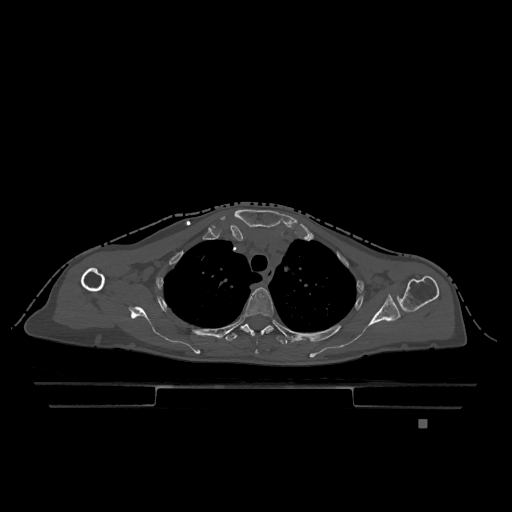
CT including the spine, one axial slice; position 908 of 1317 along the scan axis; bone window (W 1800 / L 400 HU); 0.5 mm slice thickness; 512 × 512 image matrix, field of view 500 × 500 mm. Female patient, age 74 years. From the clinical record (not read from this slice): primary cancer: lung; vertebrae with lytic lesions (as recorded): T1, T4, T5, T6, L4, L5.
Structures marked on this image (semi-automatic segmentation, software-assisted and operator-edited):
- T3 vertebra: bounding box [x1, y1, x2, y2] px = [241, 287, 274, 354]
- T4 vertebra: [225, 323, 307, 344]